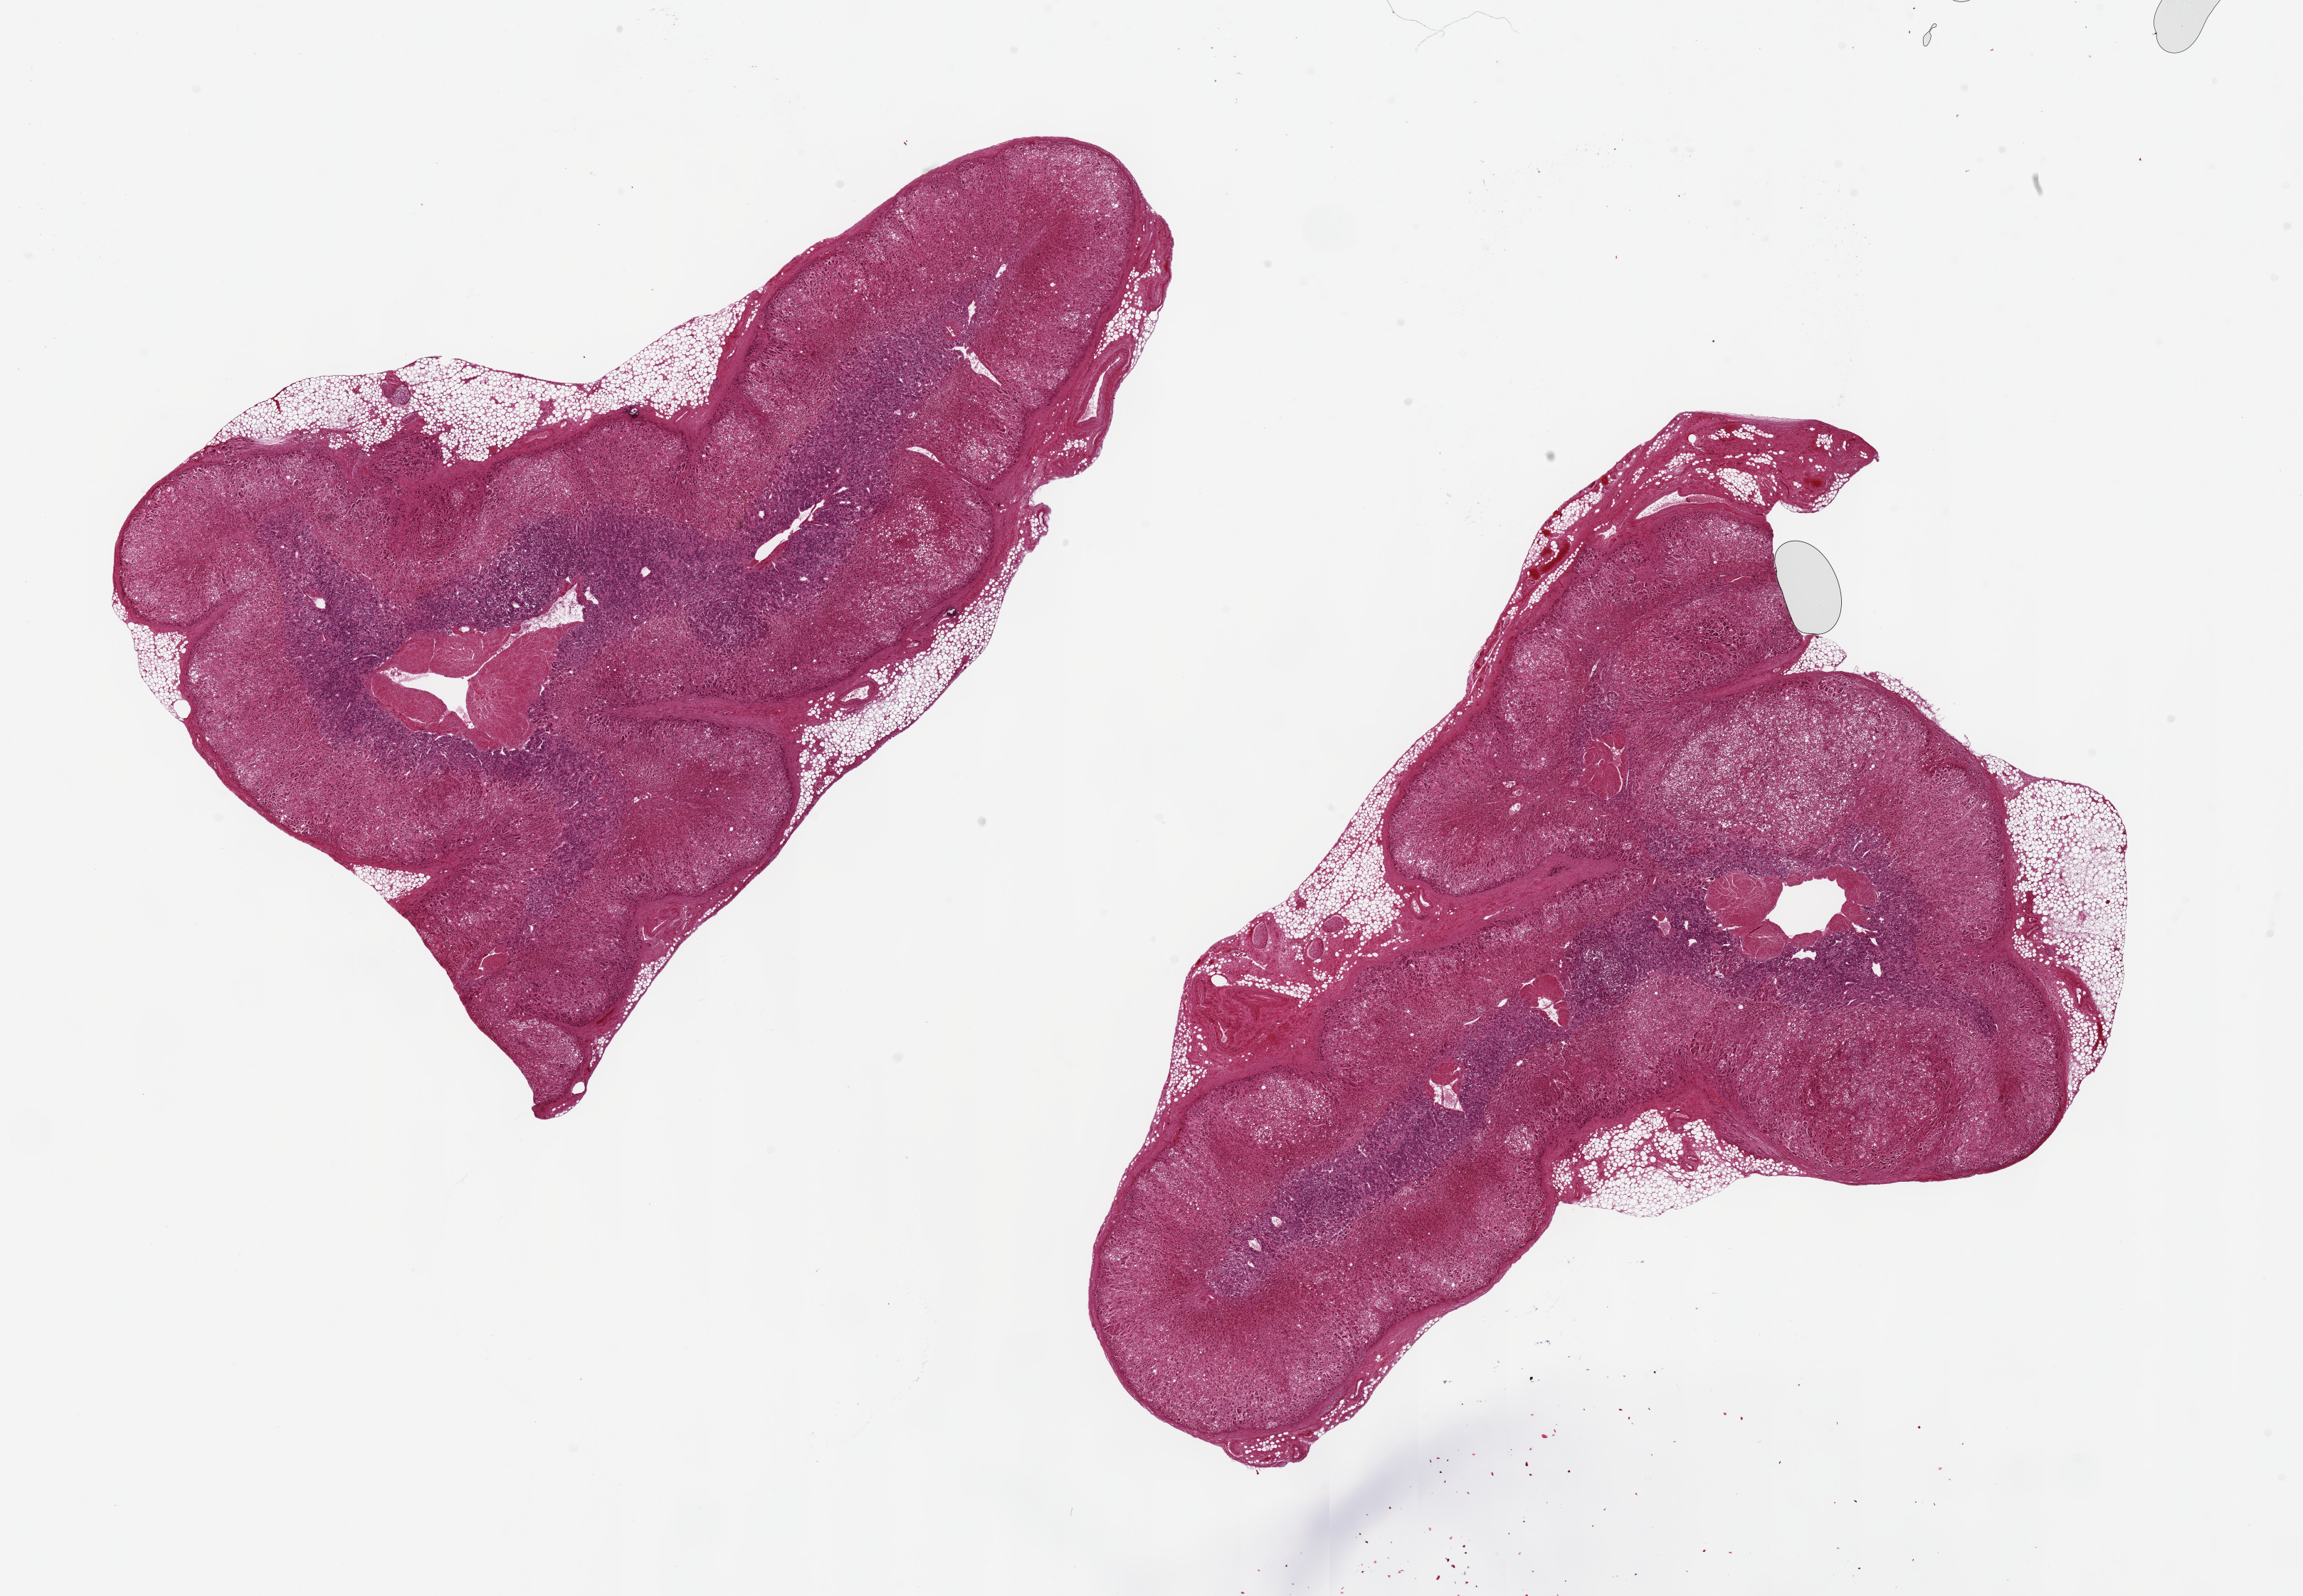
Whole-slide image, haematoxylin and eosin stain, brightfield — low-resolution overview of the scanned area, about 25.6 x 17.7 mm (from a 20x scan); PAXgene-fixed paraffin-embedded (PFPE) section; sampled site (target tissue): adrenal gland; donor tissue sample. Donor: male.
Pathologist's review note for this sample: 2 pieces badly autolyzed ~11x8mm.